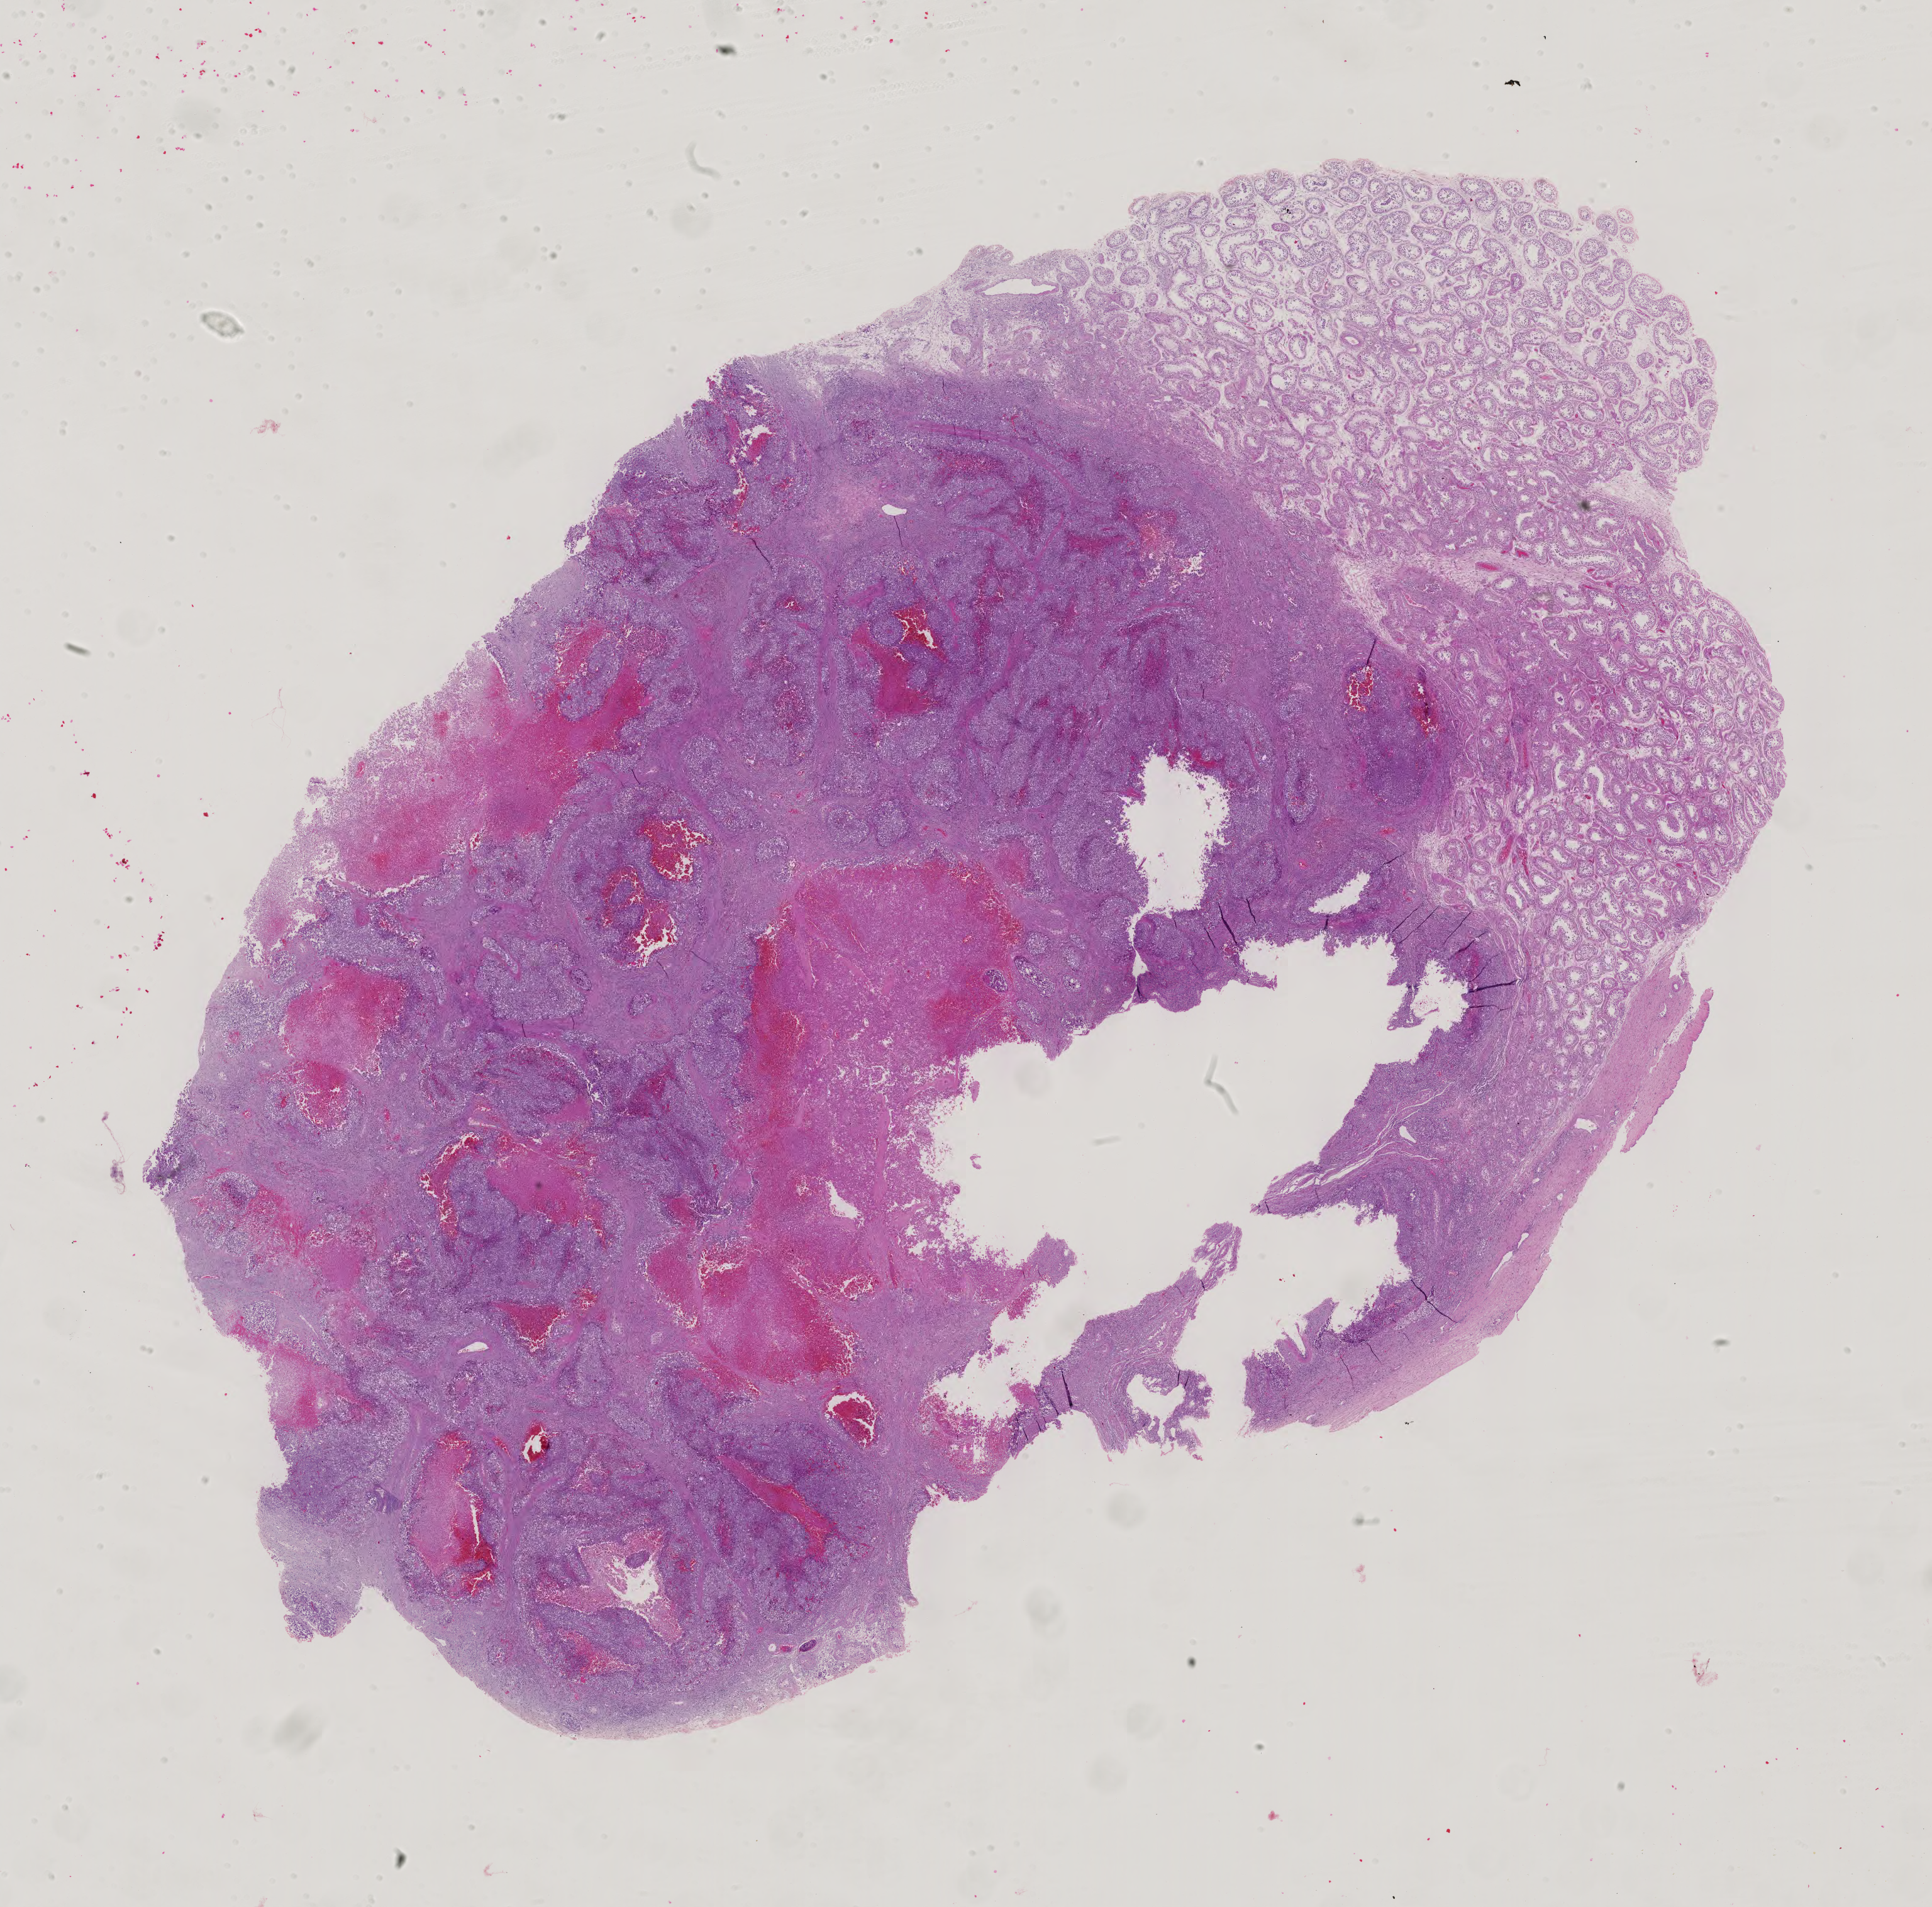
Digitized H&E tissue section (whole slide), shown as a low-resolution overview of the whole scanned area (about 22.4 x 22.1 mm, acquisition: 40x scan). Formalin-fixed paraffin-embedded (FFPE) diagnostic section. Testis, primary tumour sample. Patient: male, age at initial diagnosis 32 years.
• AJCC pathologic stage: IS (6th edition)
• pathologic diagnosis: Embryonal carcinoma, NOS